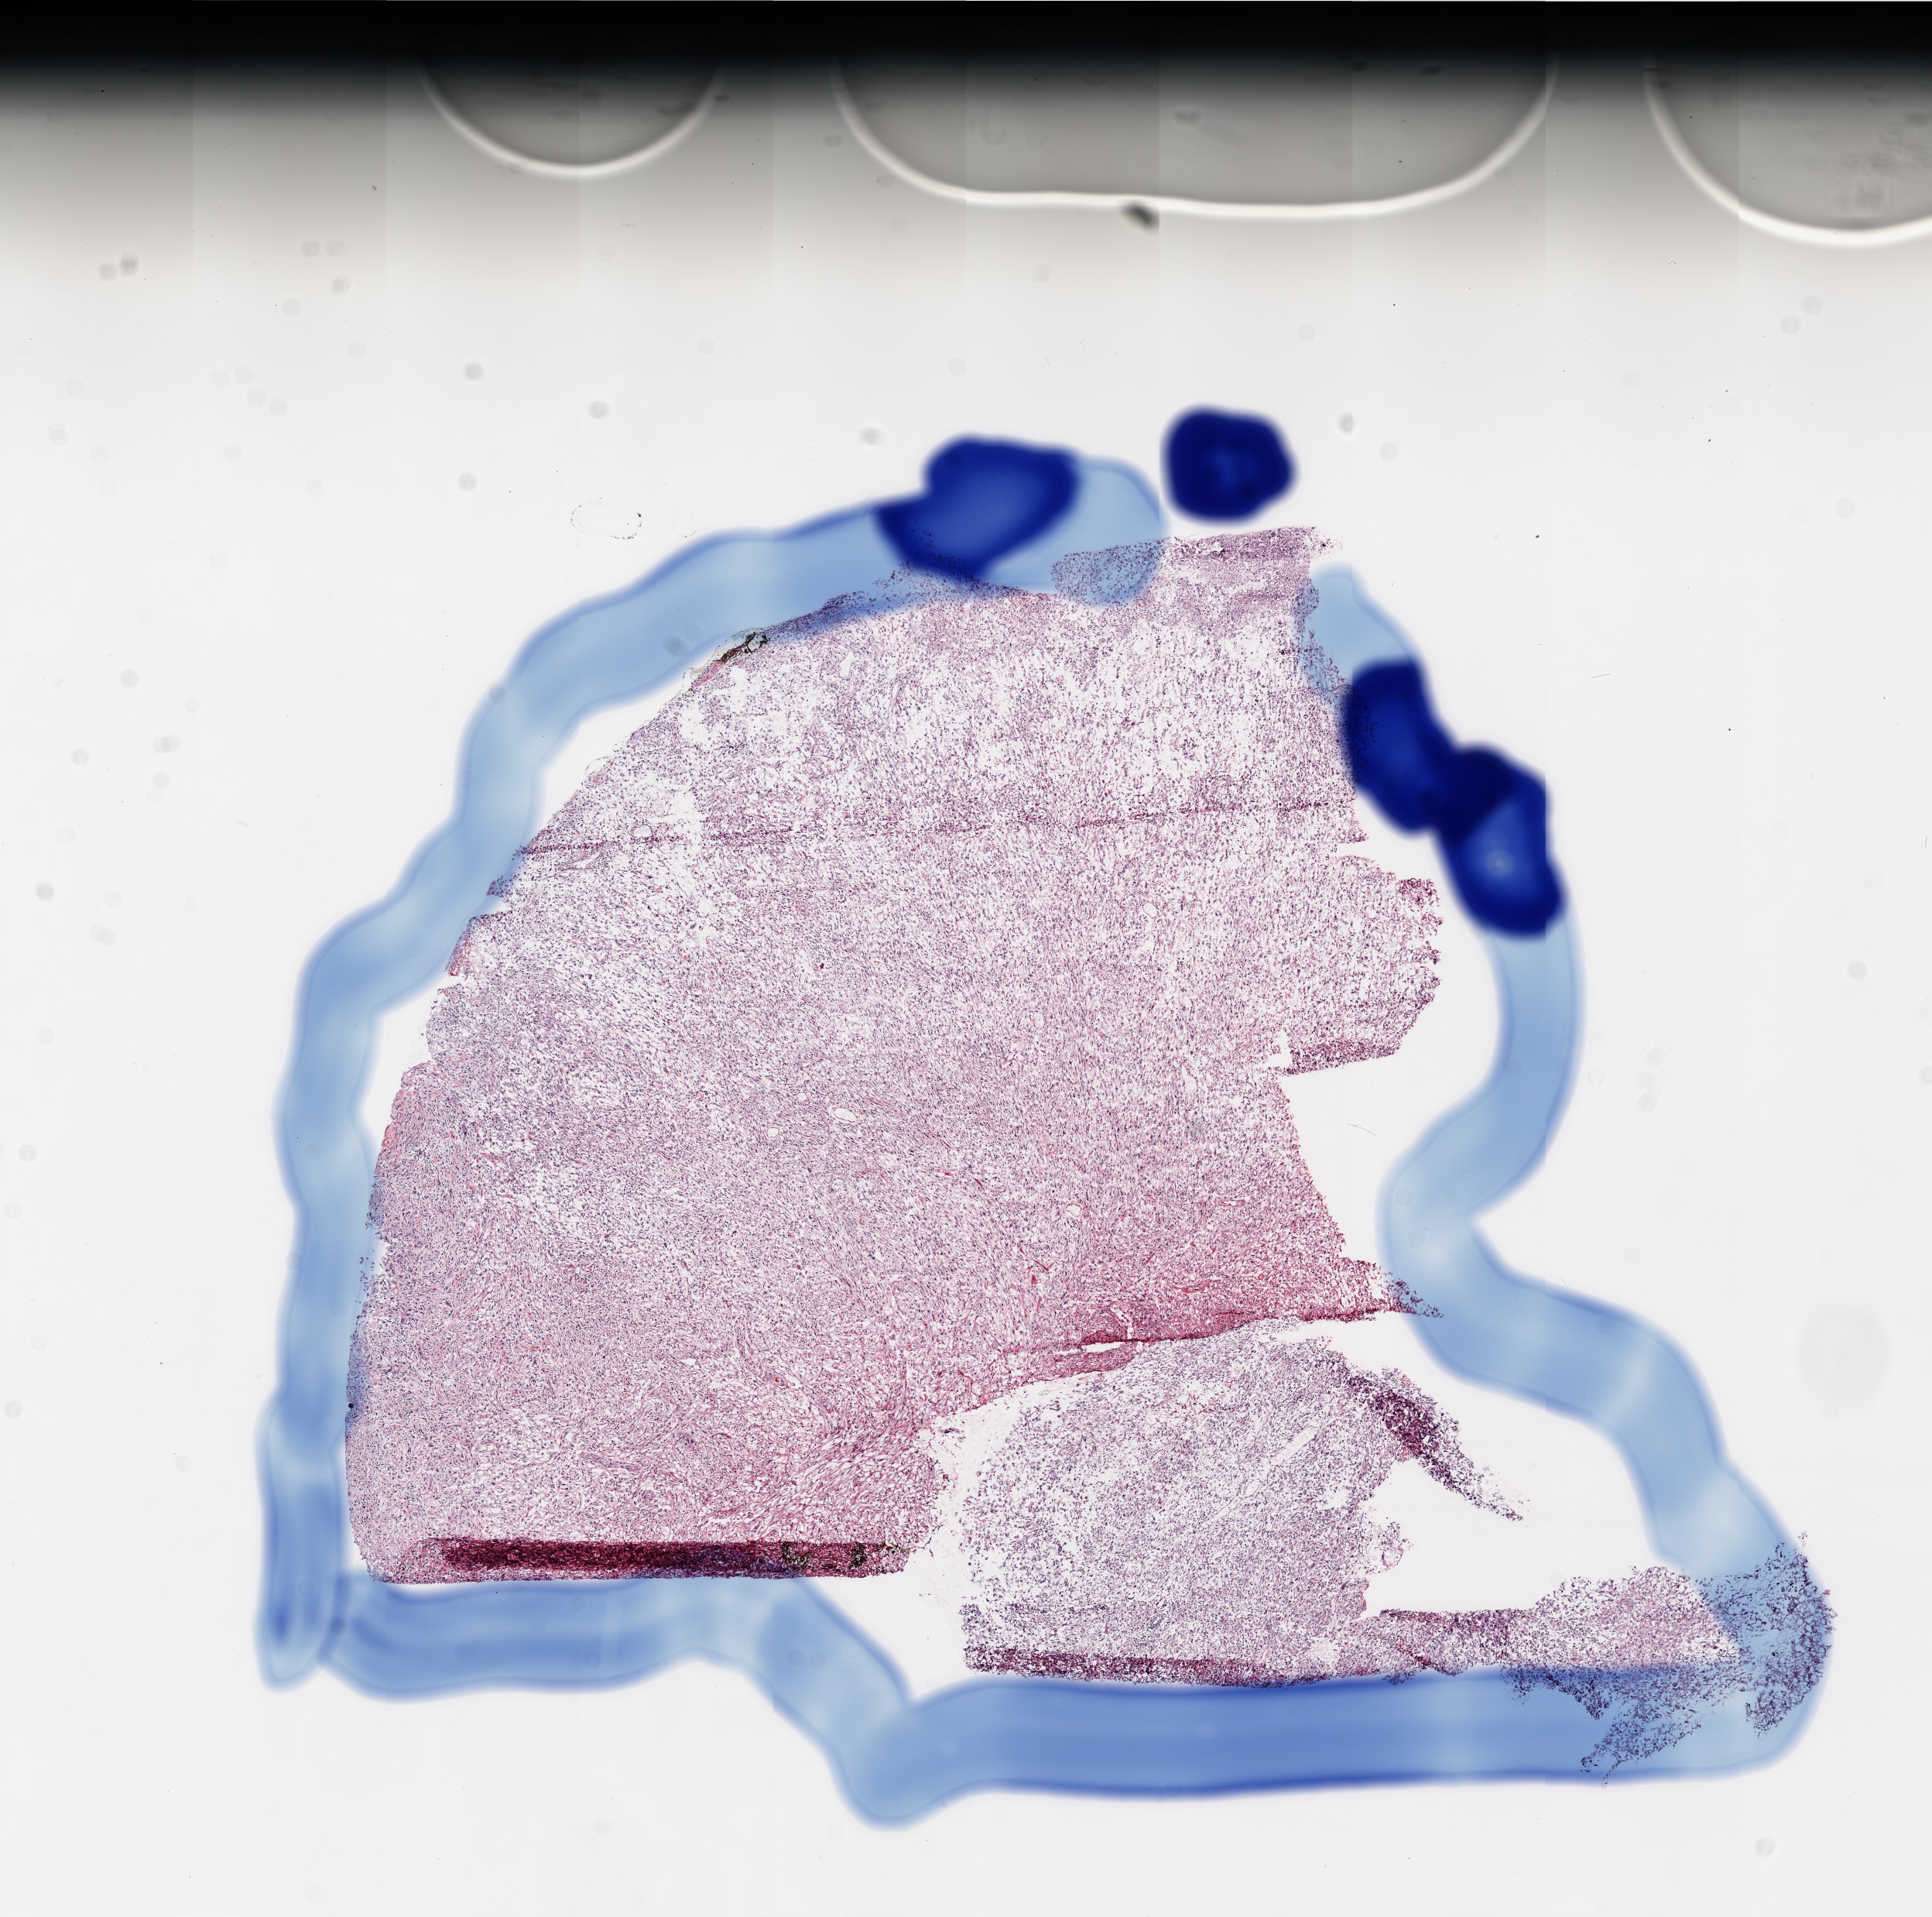
Digitized H&E-stained tissue section (whole slide) — shown as a low-resolution overview of the whole scanned area (about 10.0 x 9.9 mm); frozen section from the top of the tissue portion; primary tumour sample from the brain. Male patient; age at initial diagnosis 54 years. Pathologist review of this section (percent, as recorded): tumour cells 95%, tumour nuclei 95%, normal cells 0%, stromal cells 0%, necrosis 5%.
* histologic diagnosis: Glioblastoma